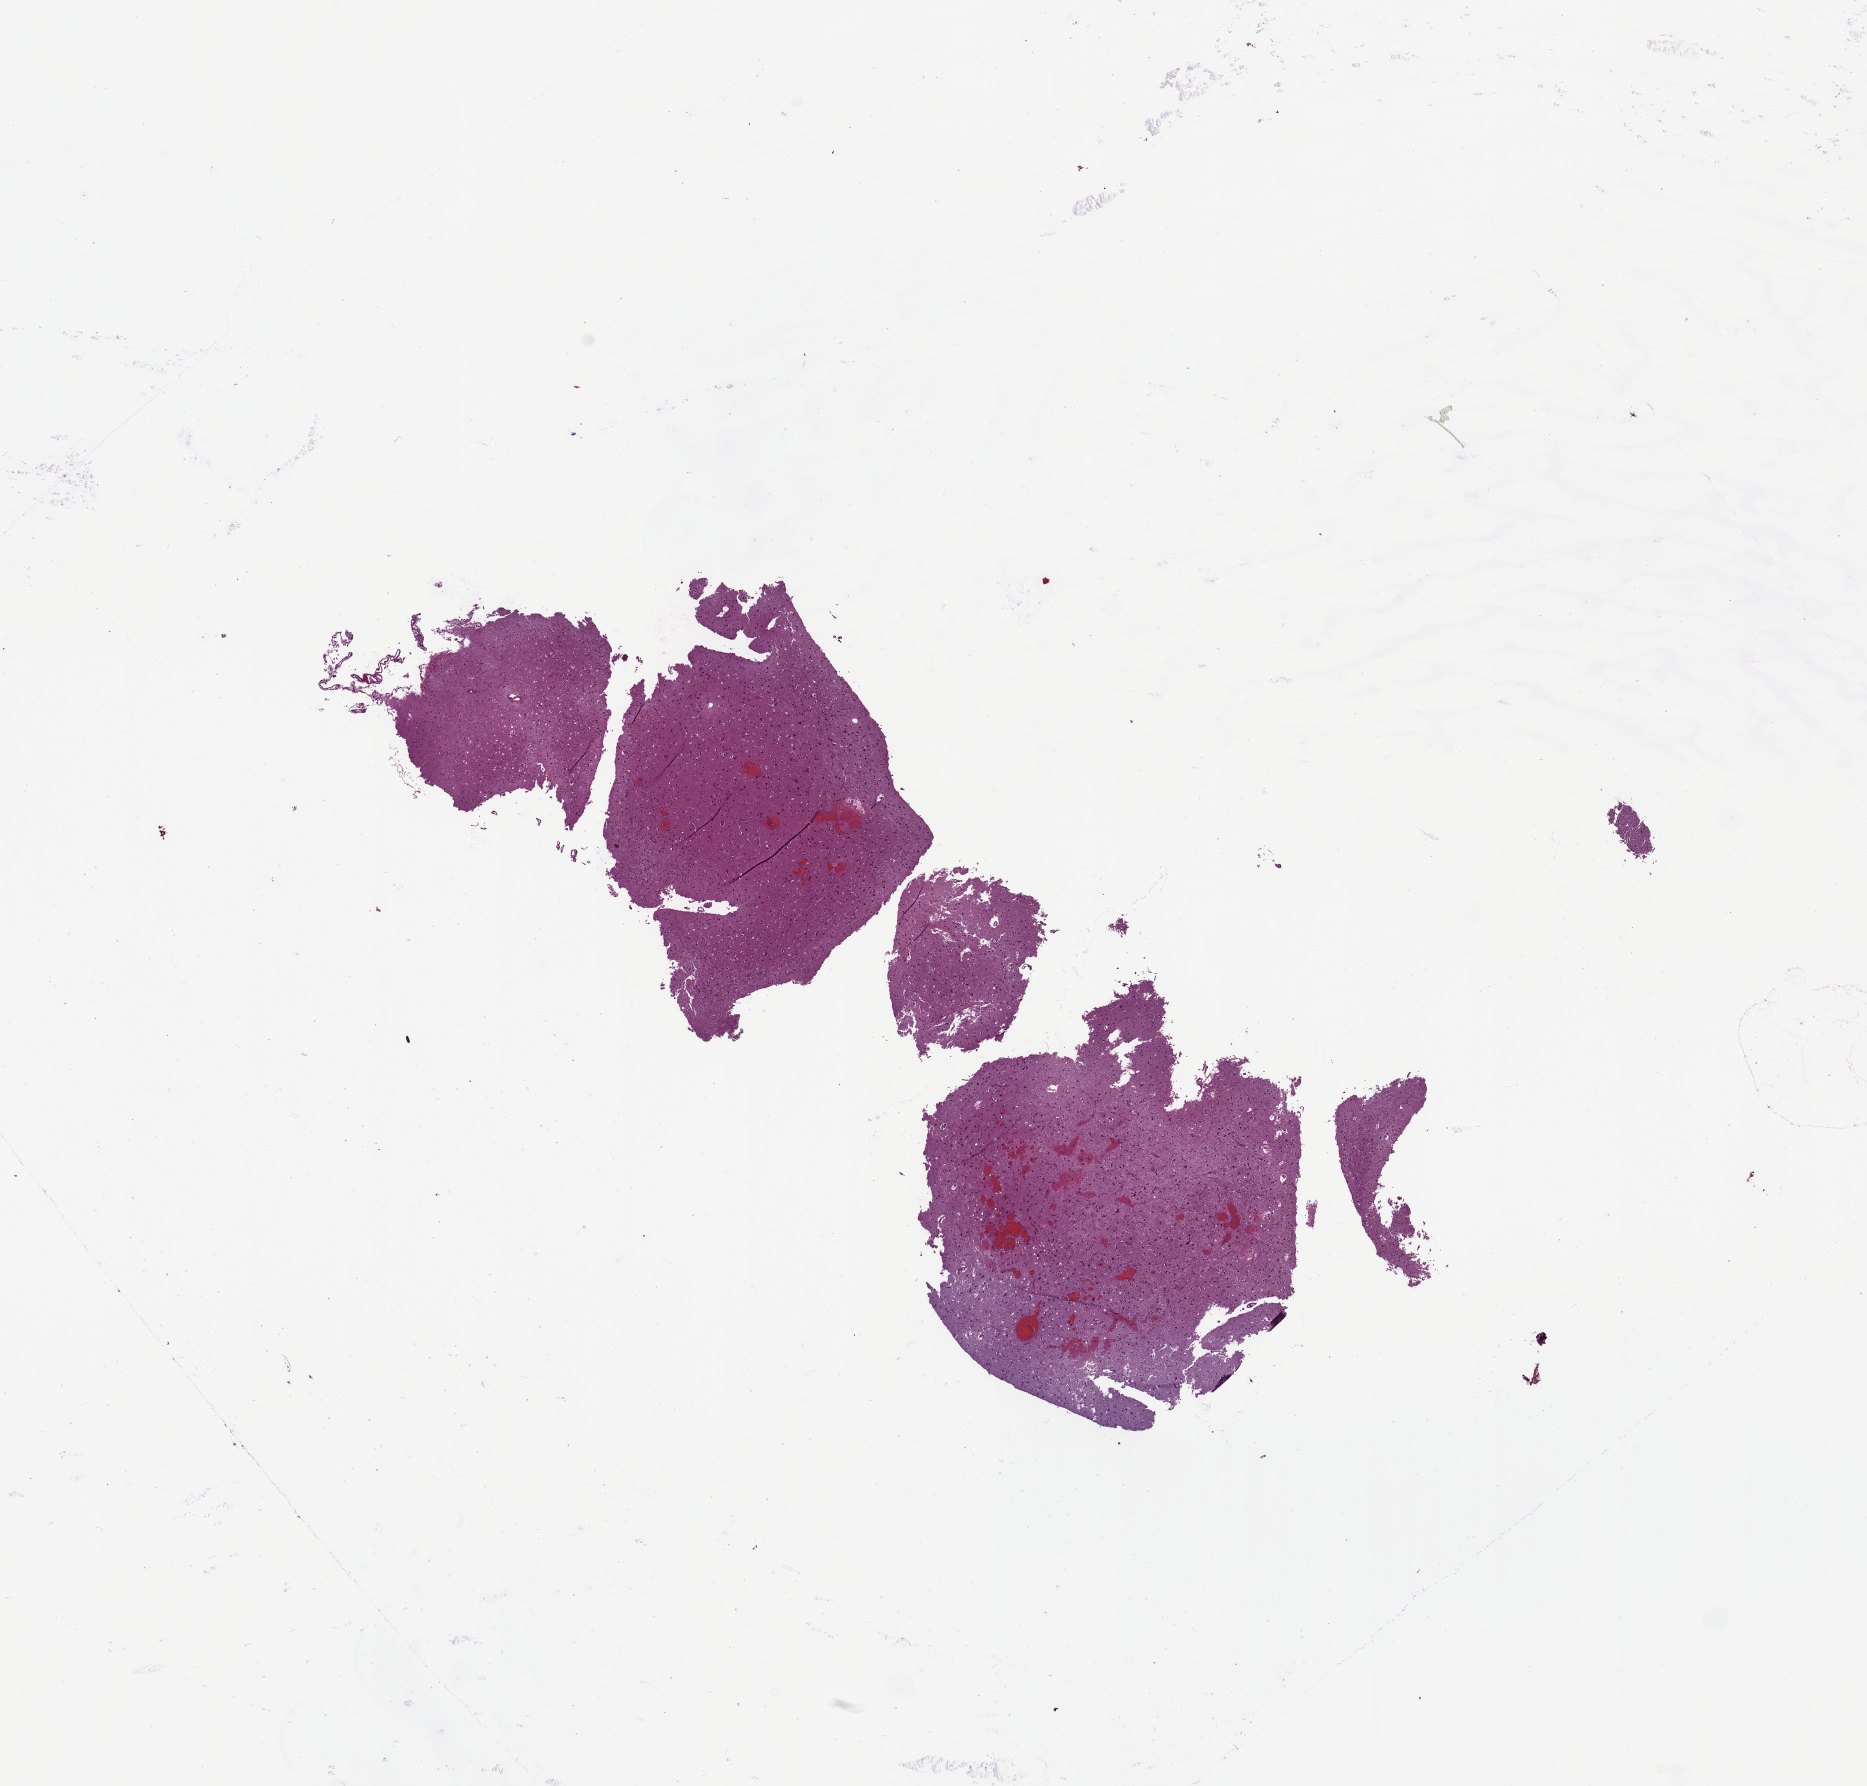
H&E whole-slide image, low-resolution overview of the scanned area, about 14.8 x 14.1 mm (slide scanned at 20x); tumour tissue sample, brain. 47-year-old male patient.
Histologic diagnosis: Glioblastoma.